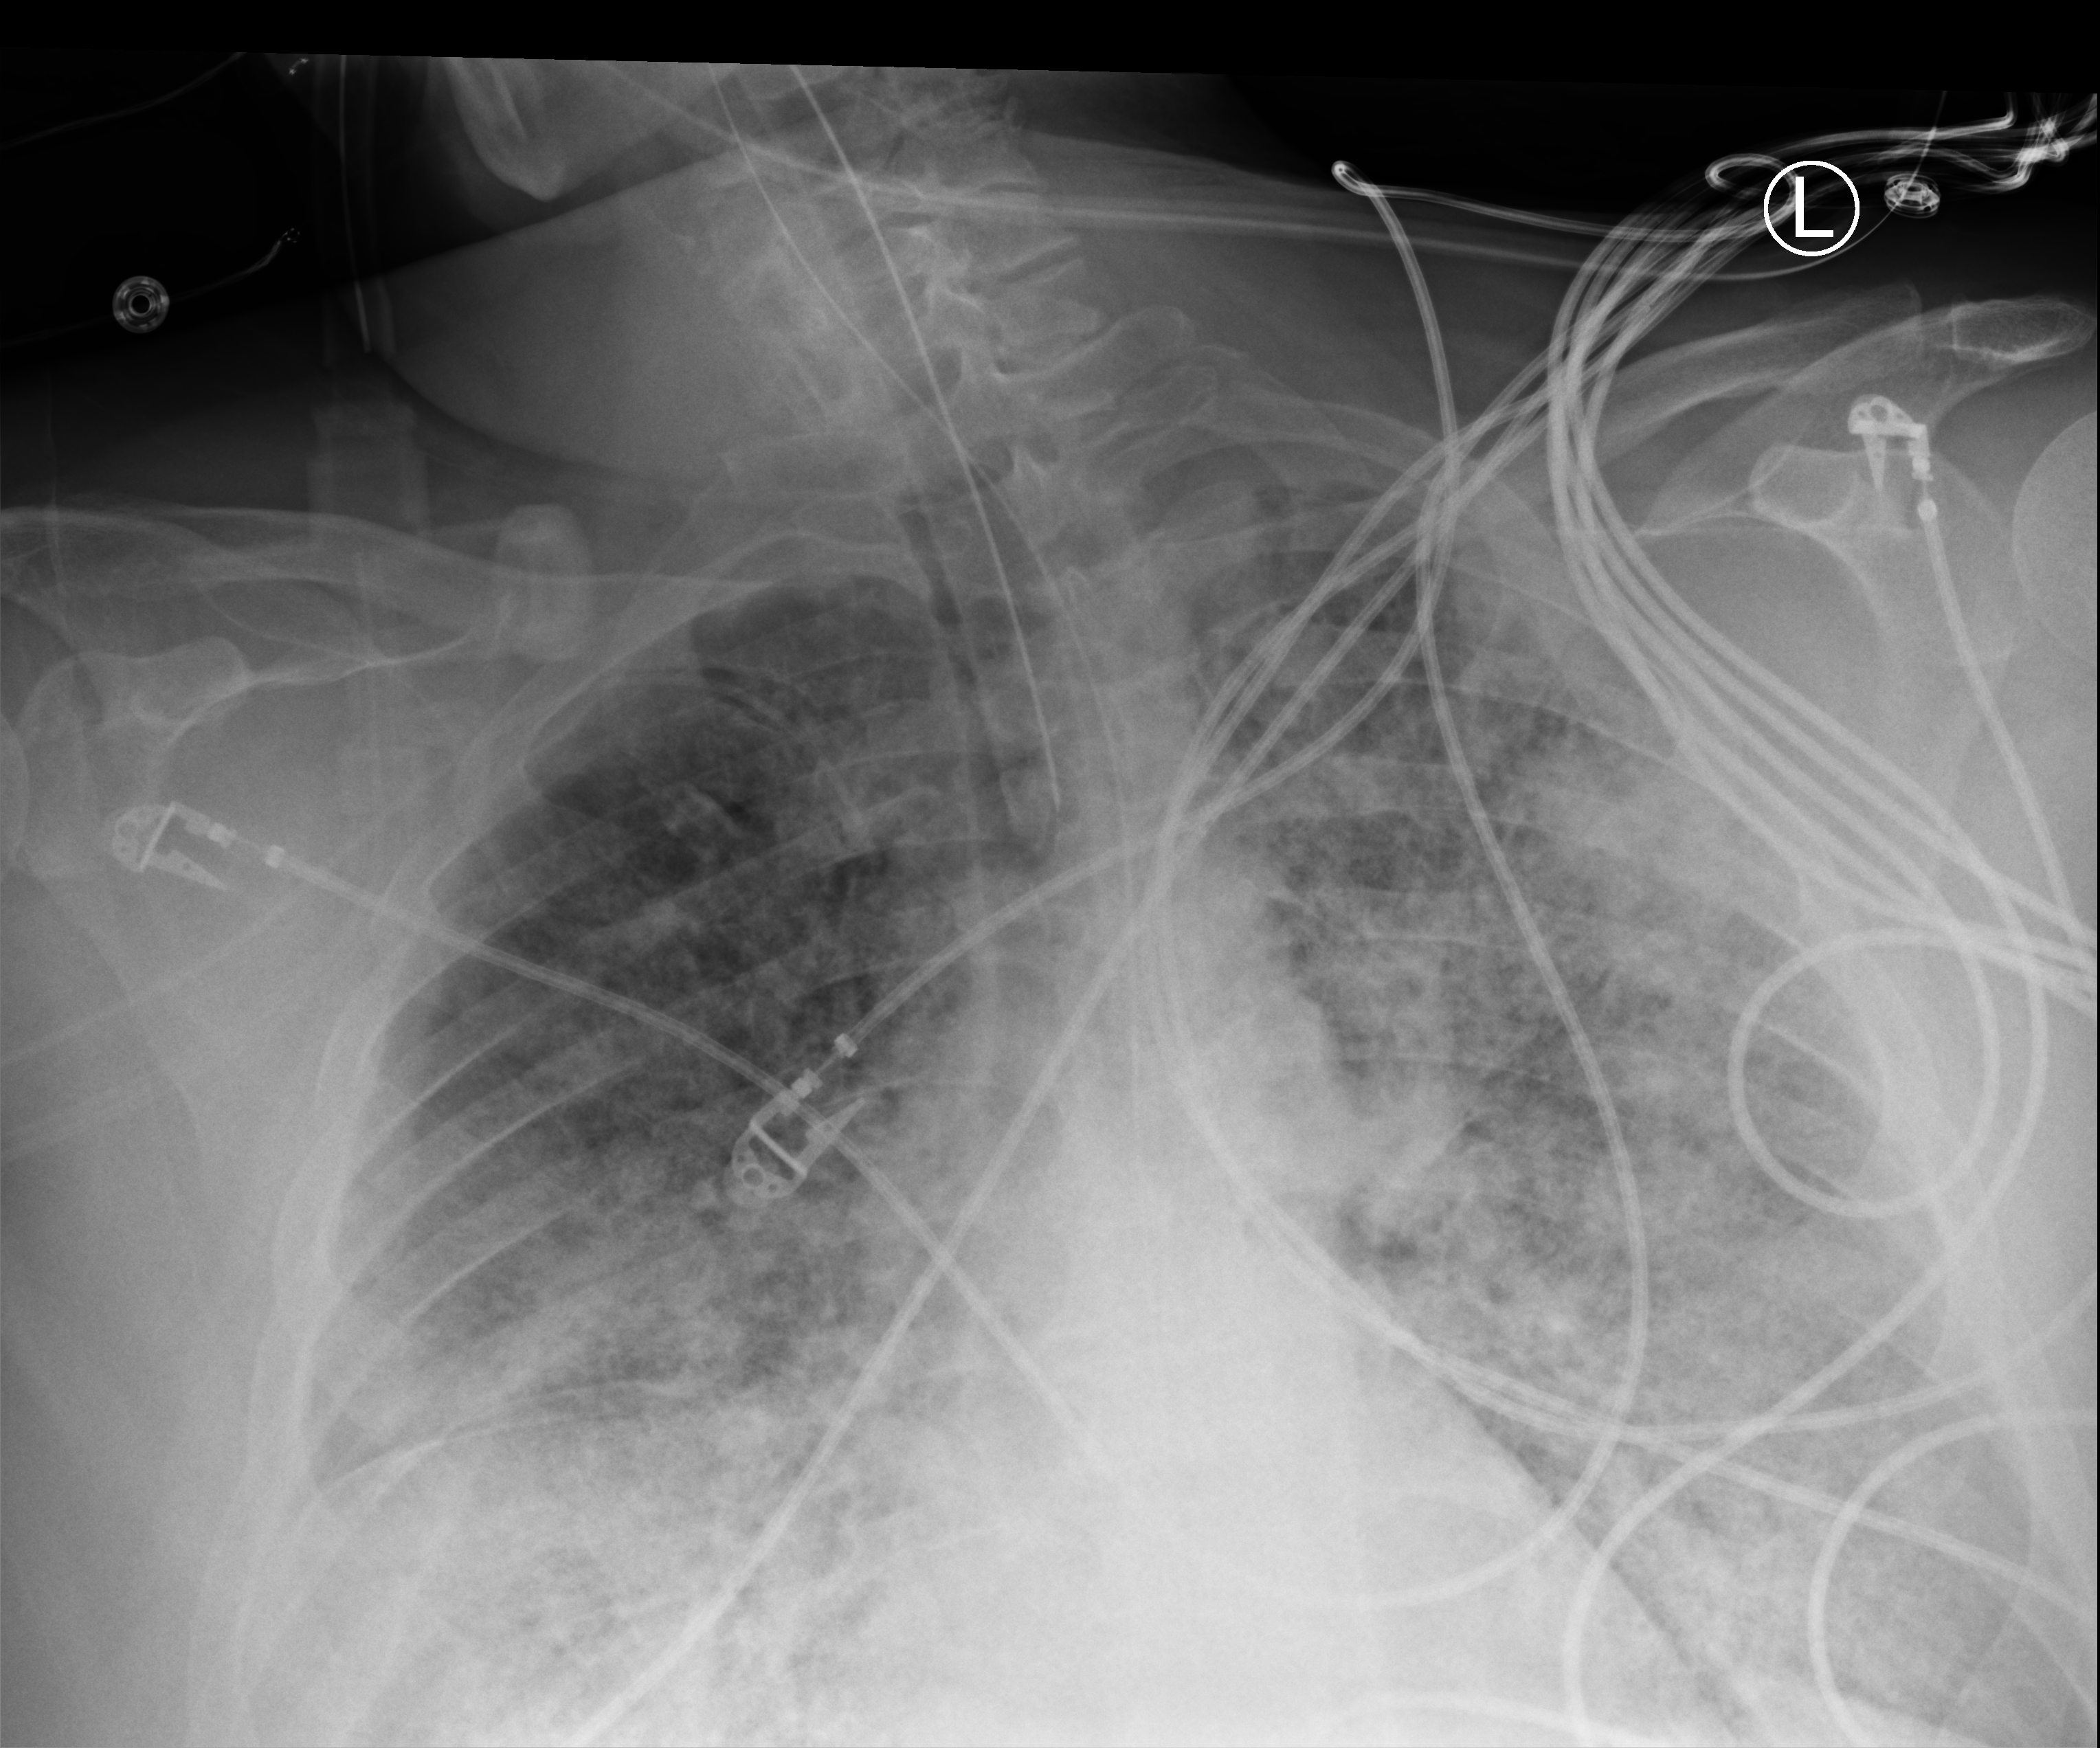
Chest X-ray (portable), anteroposterior (AP) projection. Male patient hospitalised with COVID-19, age 60–74 years.
Hospital-stay facts (about this admission, not read from this image; timing relative to this image not recorded): admitted to intensive care during this hospital stay: yes; length of hospital stay: 13 days.